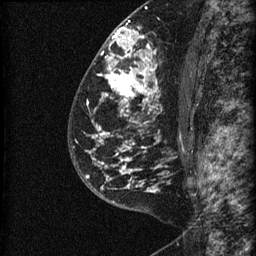
Breast MRI (dynamic contrast-enhanced), one sagittal slice; slice 40 of 60 in the series (ordered by position); dynamic contrast-enhanced series, image 2 of 3 at this slice position (ordered by acquisition); 1.5 T; TE 4.2 ms, TR 22.7 ms; 256 × 256 image matrix, field of view 180 × 180 mm. Patient: female, 48 years. From the clinical record (not read from this slice): setting: breast cancer imaged before/during neoadjuvant chemotherapy; receptor status: triple-negative.
Annotated regions visible in this slice (semi-automatically segmented with operator editing):
- analysis volume of interest (the breast-tissue region the enhancement analysis was run in; not a lesion): bounding box <81,23,186,202> (left, top, right, bottom; pixels)
- tumour enhancement mask (voxels above the 90 % enhancement threshold inside the analysis volume of interest): <86,27,158,192>